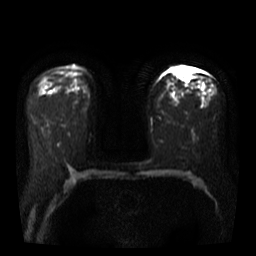
Breast MRI, one axial slice. Position 22 of 40 along the scan axis. Diffusion-weighted series; image 2 of 4 stored at this slice position (different b-values; order by instance number). 3 T. 5 mm slice thickness. 256 × 256 image matrix. Female patient.
Outlined on this slice (manually delineated by an expert):
- tumour on diffusion-weighted imaging: box from (x=175, y=68) to (x=191, y=83) px